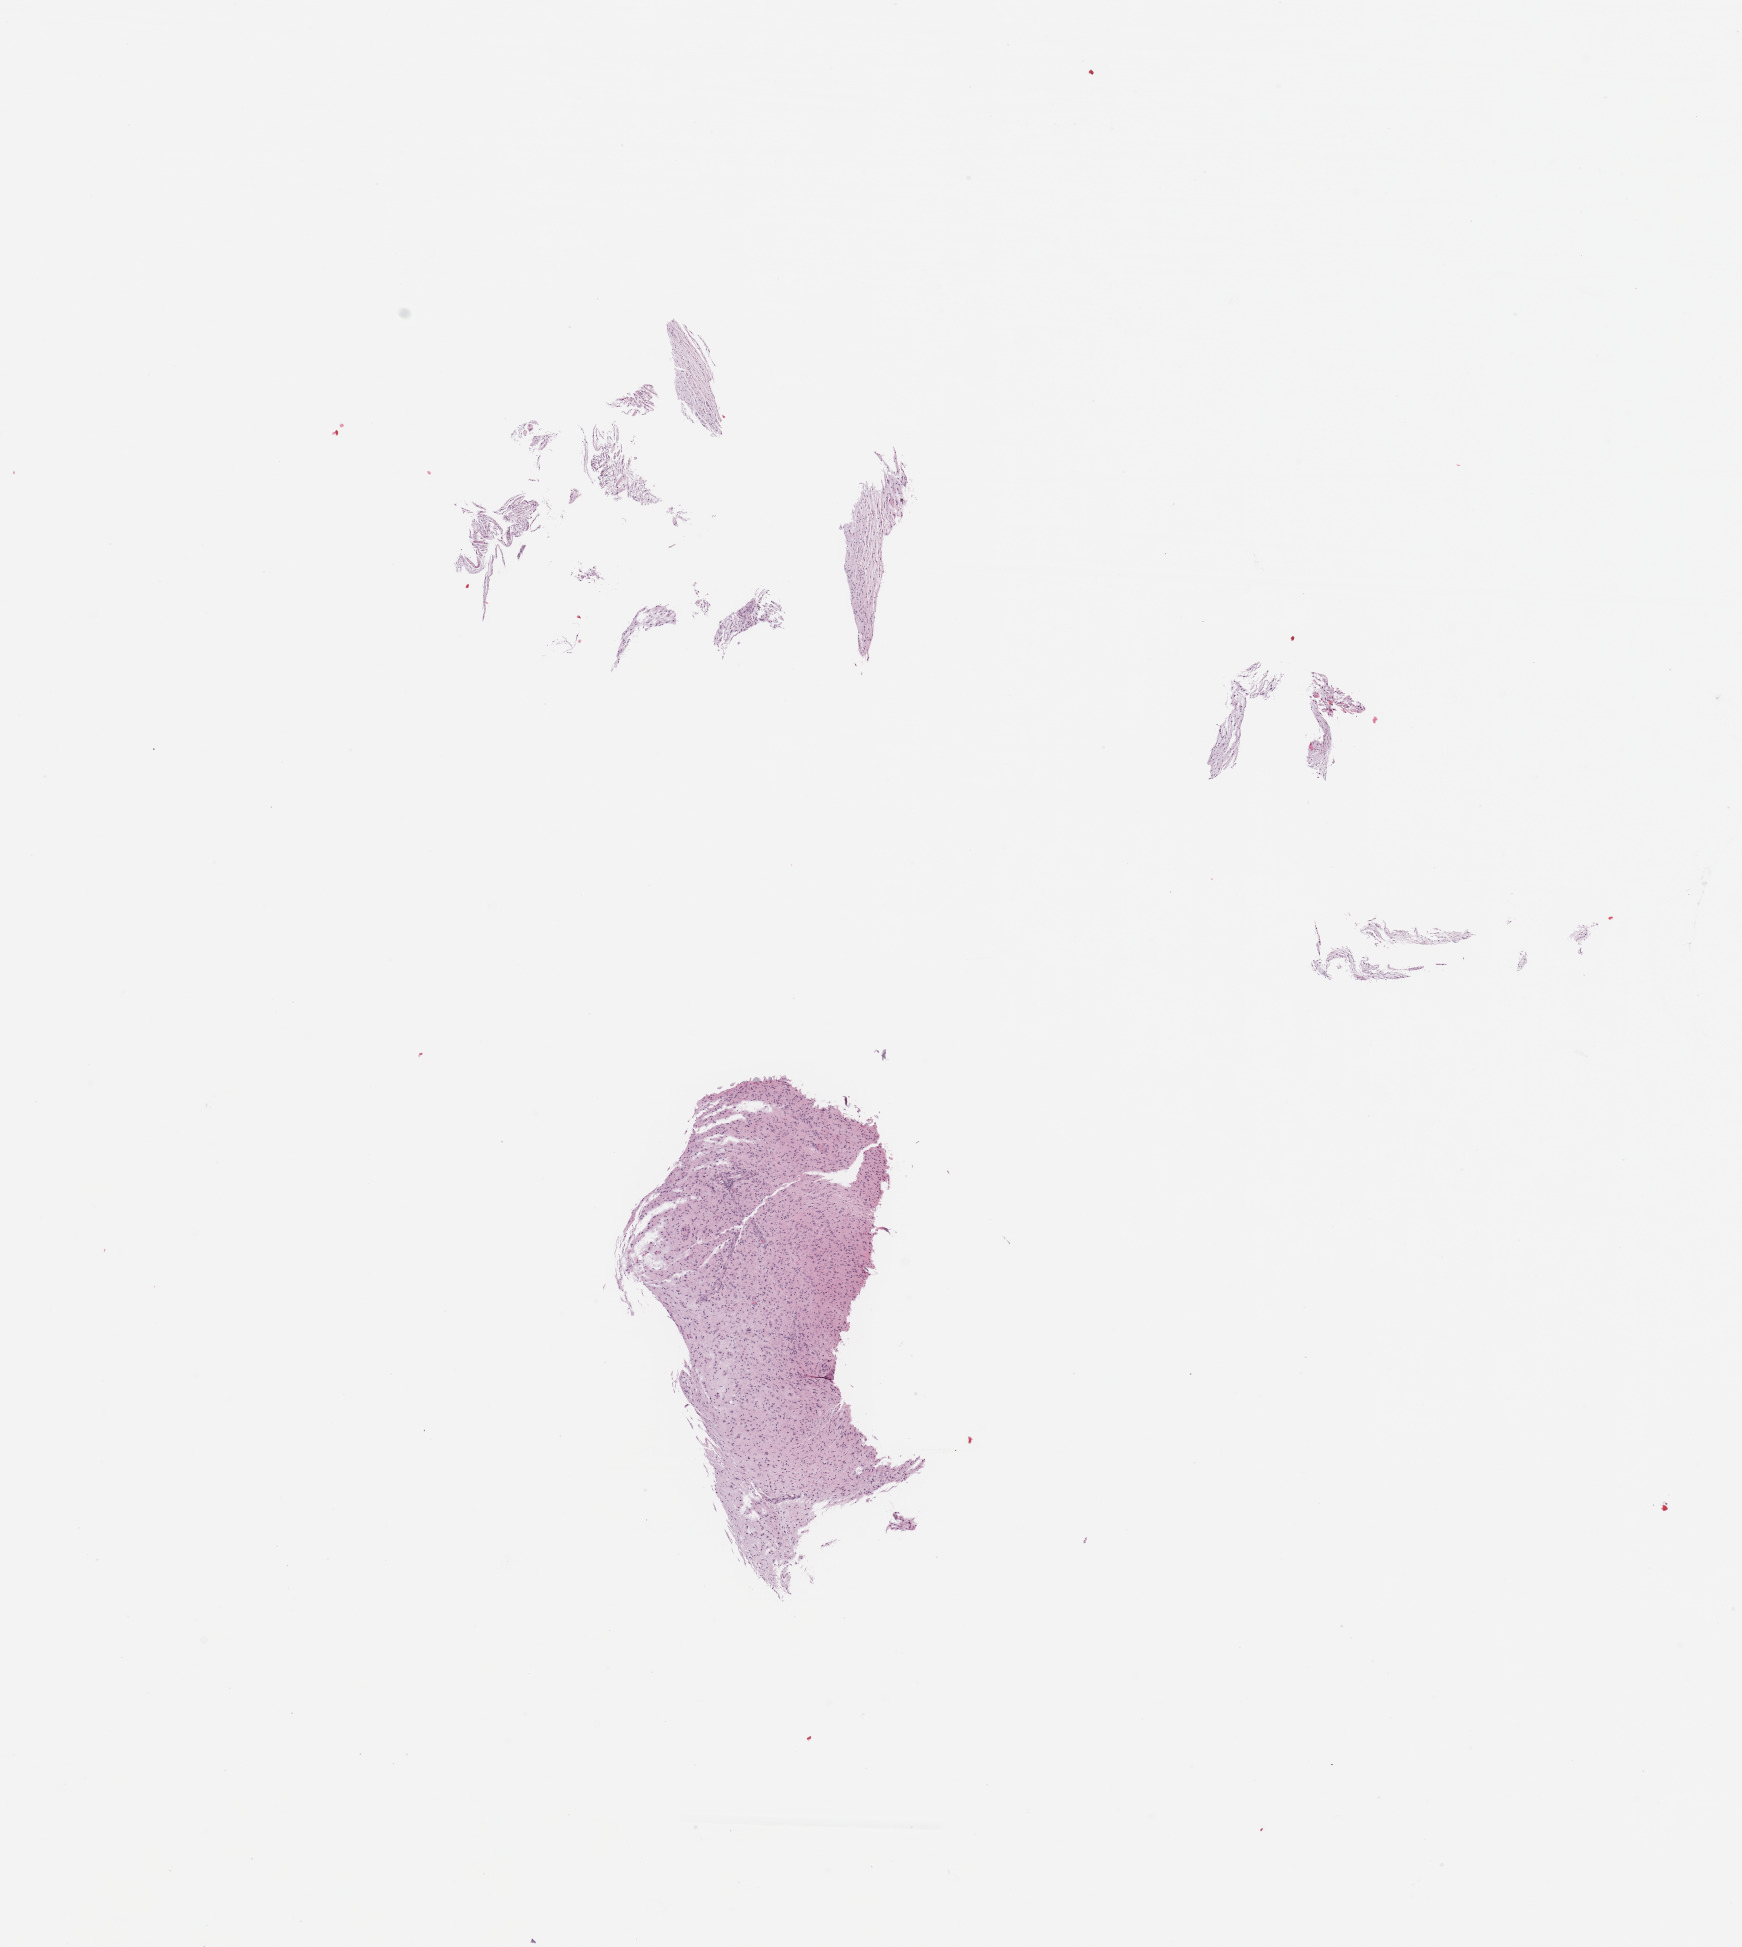
Digitized H&E tissue section (whole slide), whole scanned area (about 13.8 x 15.4 mm) shown as a low-resolution overview; tumour tissue sample, sampled site: frontal lobe. Female, 57 y/o. Composition of this section per pathologist review: tumour nuclei 70%, necrosis 5%.
Diagnosis: Glioblastoma.